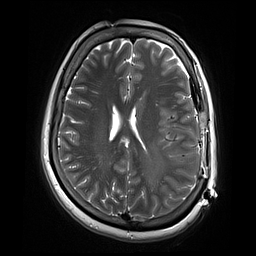
Brain MRI from a brain-tumour surgery series, one axial slice. 2 mm slice thickness. 256 × 256 image matrix, field of view 220 × 220 mm. From the clinical record (not read from this slice): histopathology: Glioblastoma; WHO grade: 4; IDH mutation: no; tumour location: Left Temporal.
Outlined on this slice (outlined manually by an expert reader):
- residual tumour: bounding box <159,116,173,131> (left, top, right, bottom; pixels)